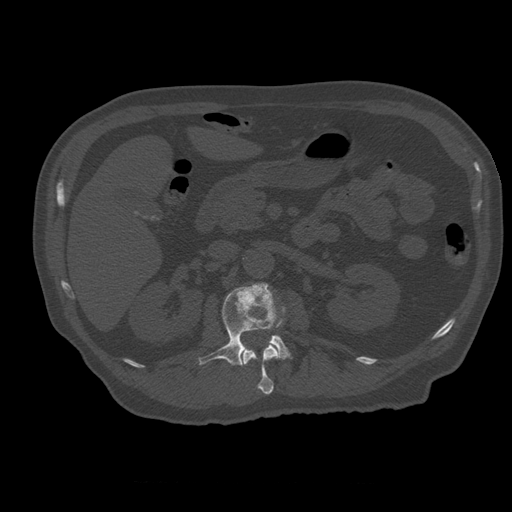
CT including the spine, one axial slice. Position 223 of 399 along the scan axis. Bone window (W 1800 / L 400 HU). 1.25 mm slice thickness. 512 × 512 image matrix. Patient age 73 years. Case-level facts recorded for this patient, not image findings: primary cancer: prostate; vertebrae with lytic lesions (as recorded): L2.
Outlined on this slice (semi-automatic segmentation, software-assisted and operator-edited):
- L1 vertebra: bounding box [x1, y1, x2, y2] px = [241, 341, 281, 395]
- L2 vertebra: [199, 283, 292, 366]